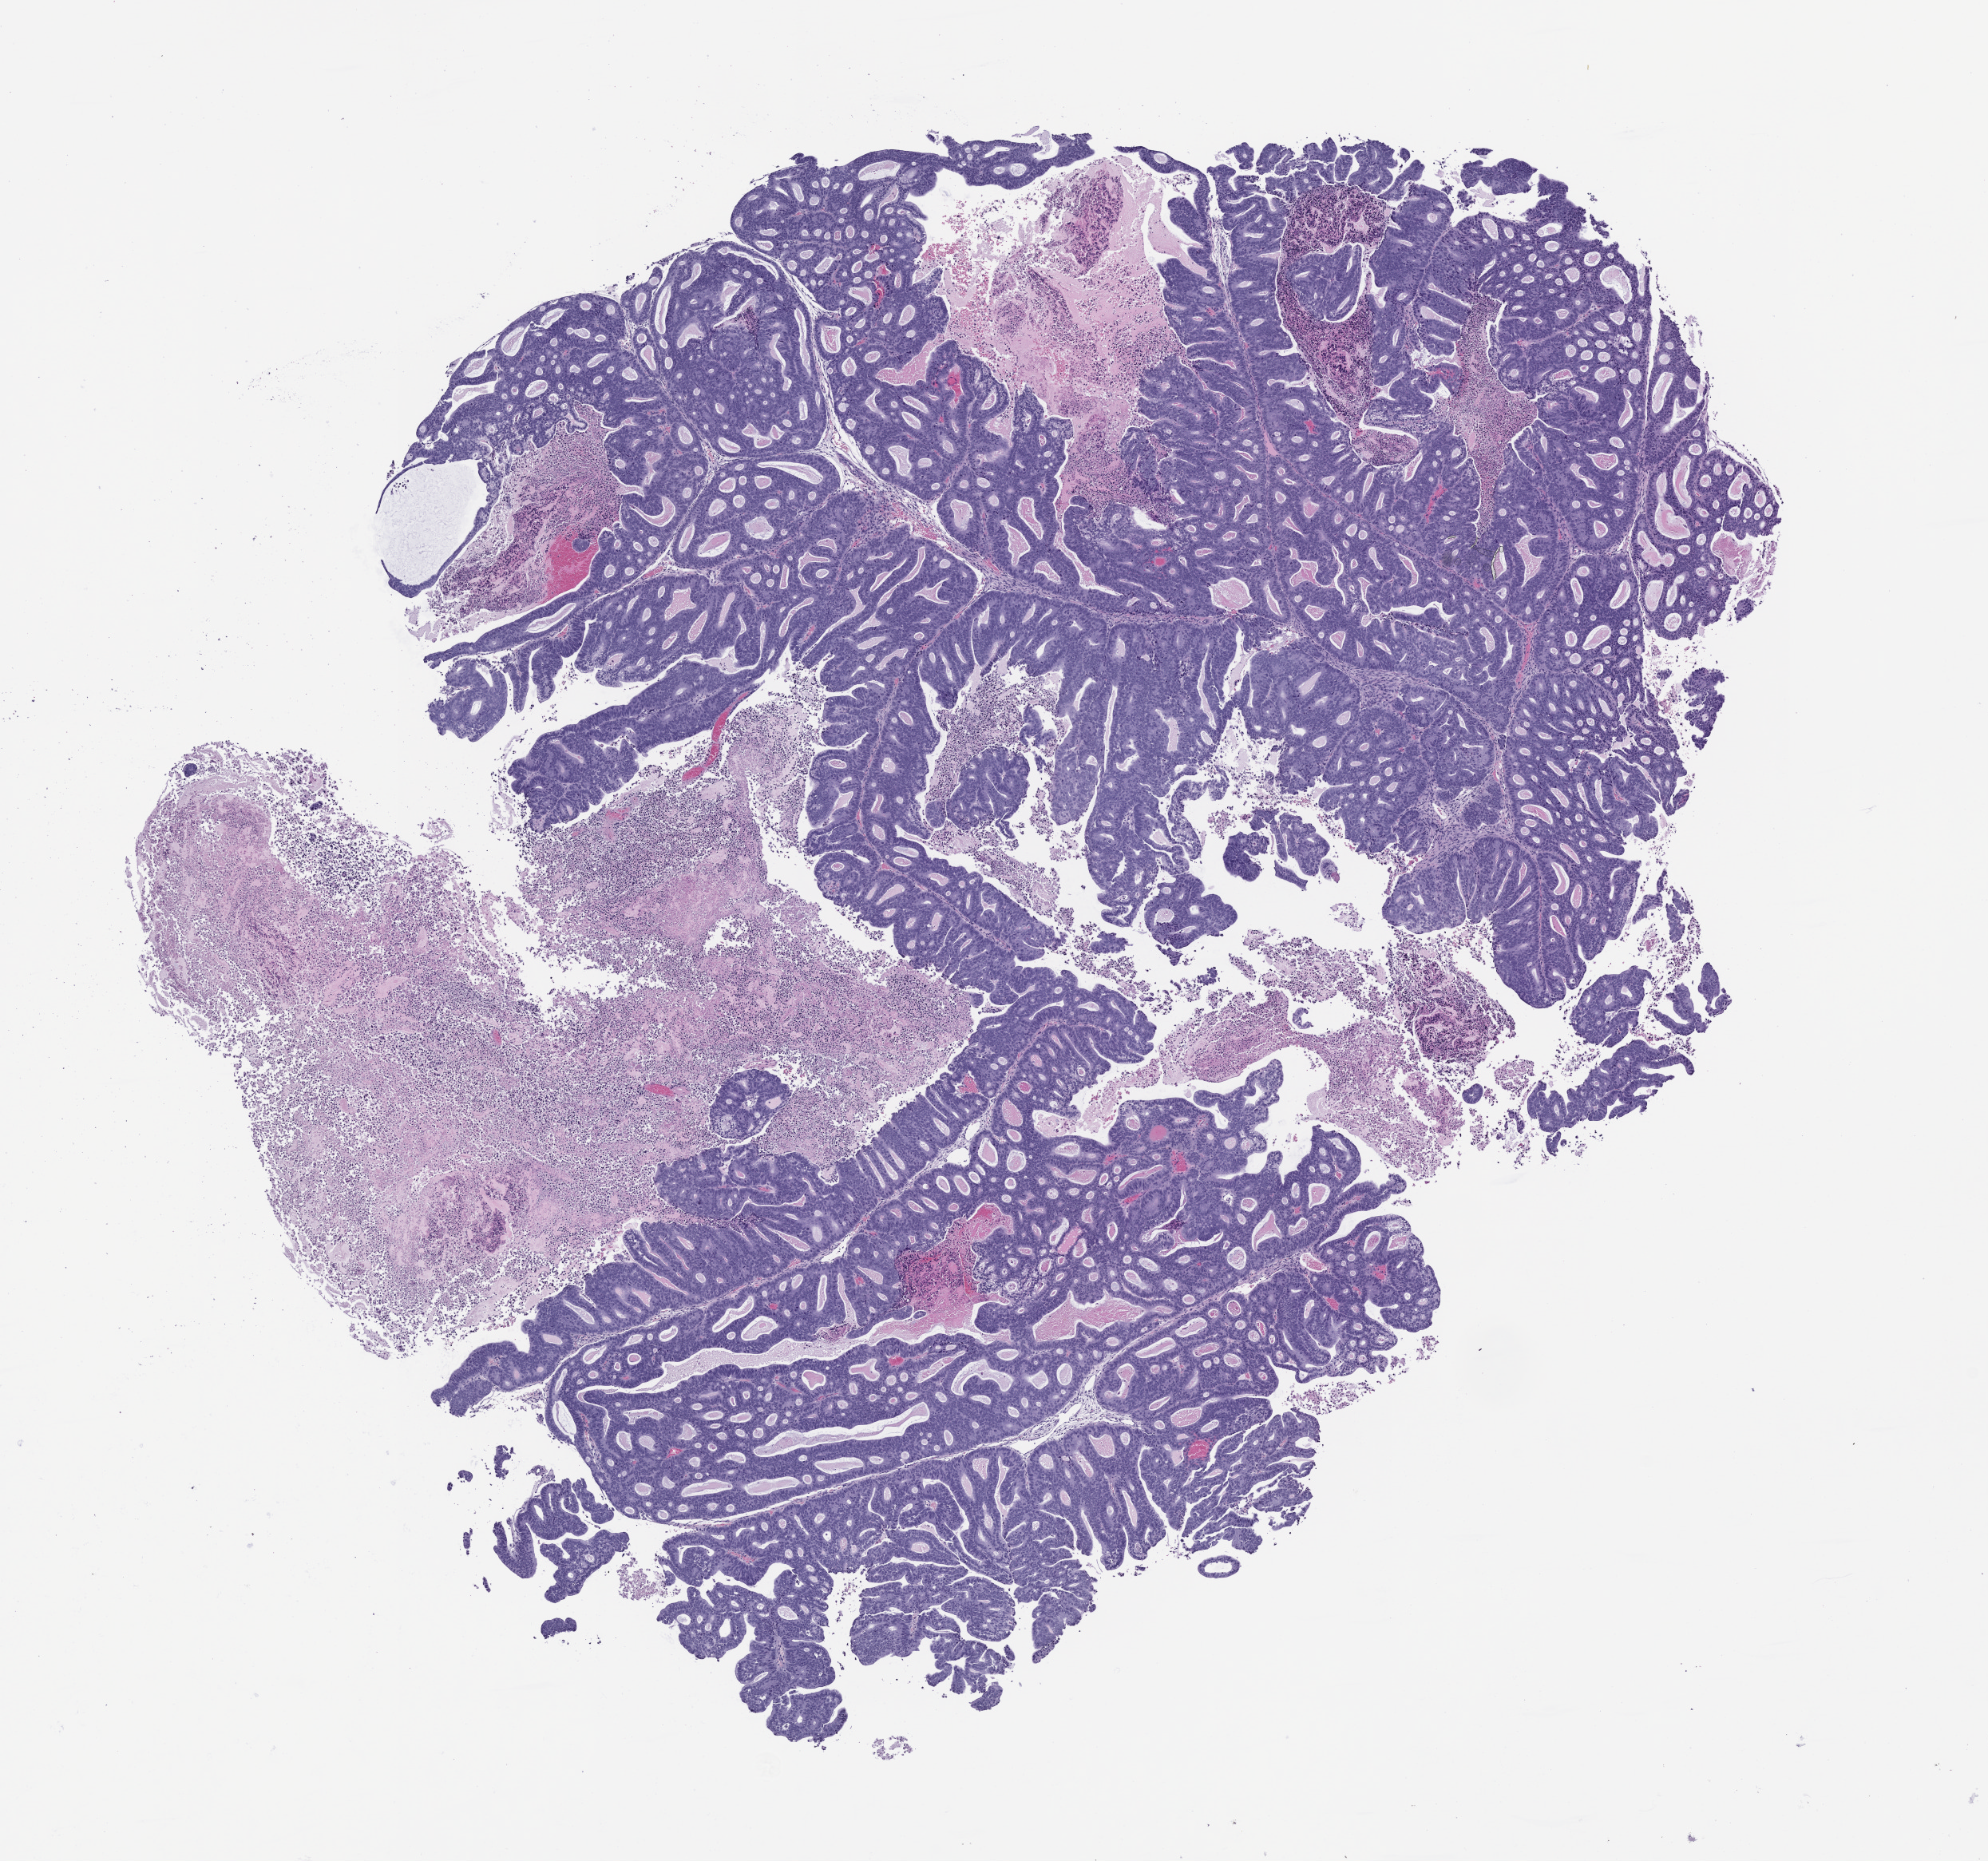
Whole-slide image, haematoxylin and eosin: patient-derived xenograft (human tumor grown in a mouse), passage 1, a low-resolution overview of the entire scanned area, about 10.0 x 9.4 mm; formalin-fixed, paraffin-embedded (FFPE) tissue; tumor site category: colon.
Originating patient diagnosis: Colon Adenocarcinoma.